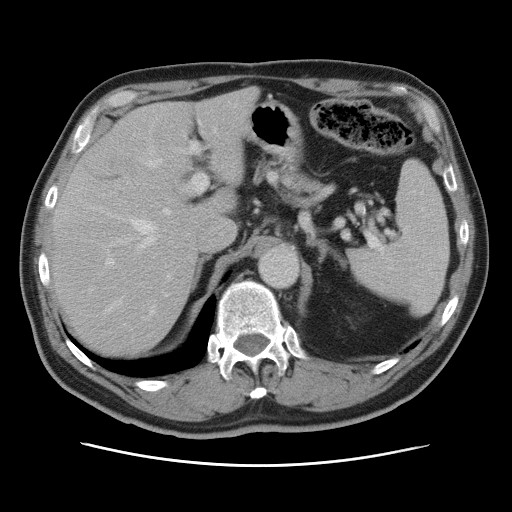
Contrast-enhanced abdominal CT, one axial slice; slice 54 of 80 in the series (ordered by position); intravenous contrast given; soft-tissue window (W 400 / L 40 HU); 5 mm slice thickness; 512 × 512 image matrix. Male patient, age 69 years. Case-level facts recorded for this patient, not image findings: diagnosis: colorectal cancer liver metastases, imaged before liver resection; multiple liver metastases: no; largest metastasis: 5 cm; chemotherapy before resection: no.
Structures marked on this image (outlined manually by an expert reader):
- hepatic veins: bounding box <107,158,163,314> (left, top, right, bottom; pixels)
- liver: <53,91,254,358>
- planned liver remnant (the part of the liver to remain after resection): <52,91,253,358>
- portal vein (with intrahepatic branches): <103,127,217,280>
- liver metastasis: <110,165,113,168>